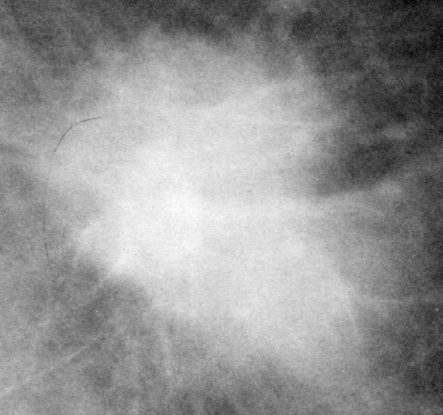
Crop from a digitized film mammogram around one marked abnormality; left breast; MLO view.
- Marked abnormality: mass, shape irregular, margins spiculated; BI-RADS assessment category 5; subtlety rating 5 on a 1 (subtle) to 5 (obvious) scale; pathology result (as recorded, not read from the image): malignant.